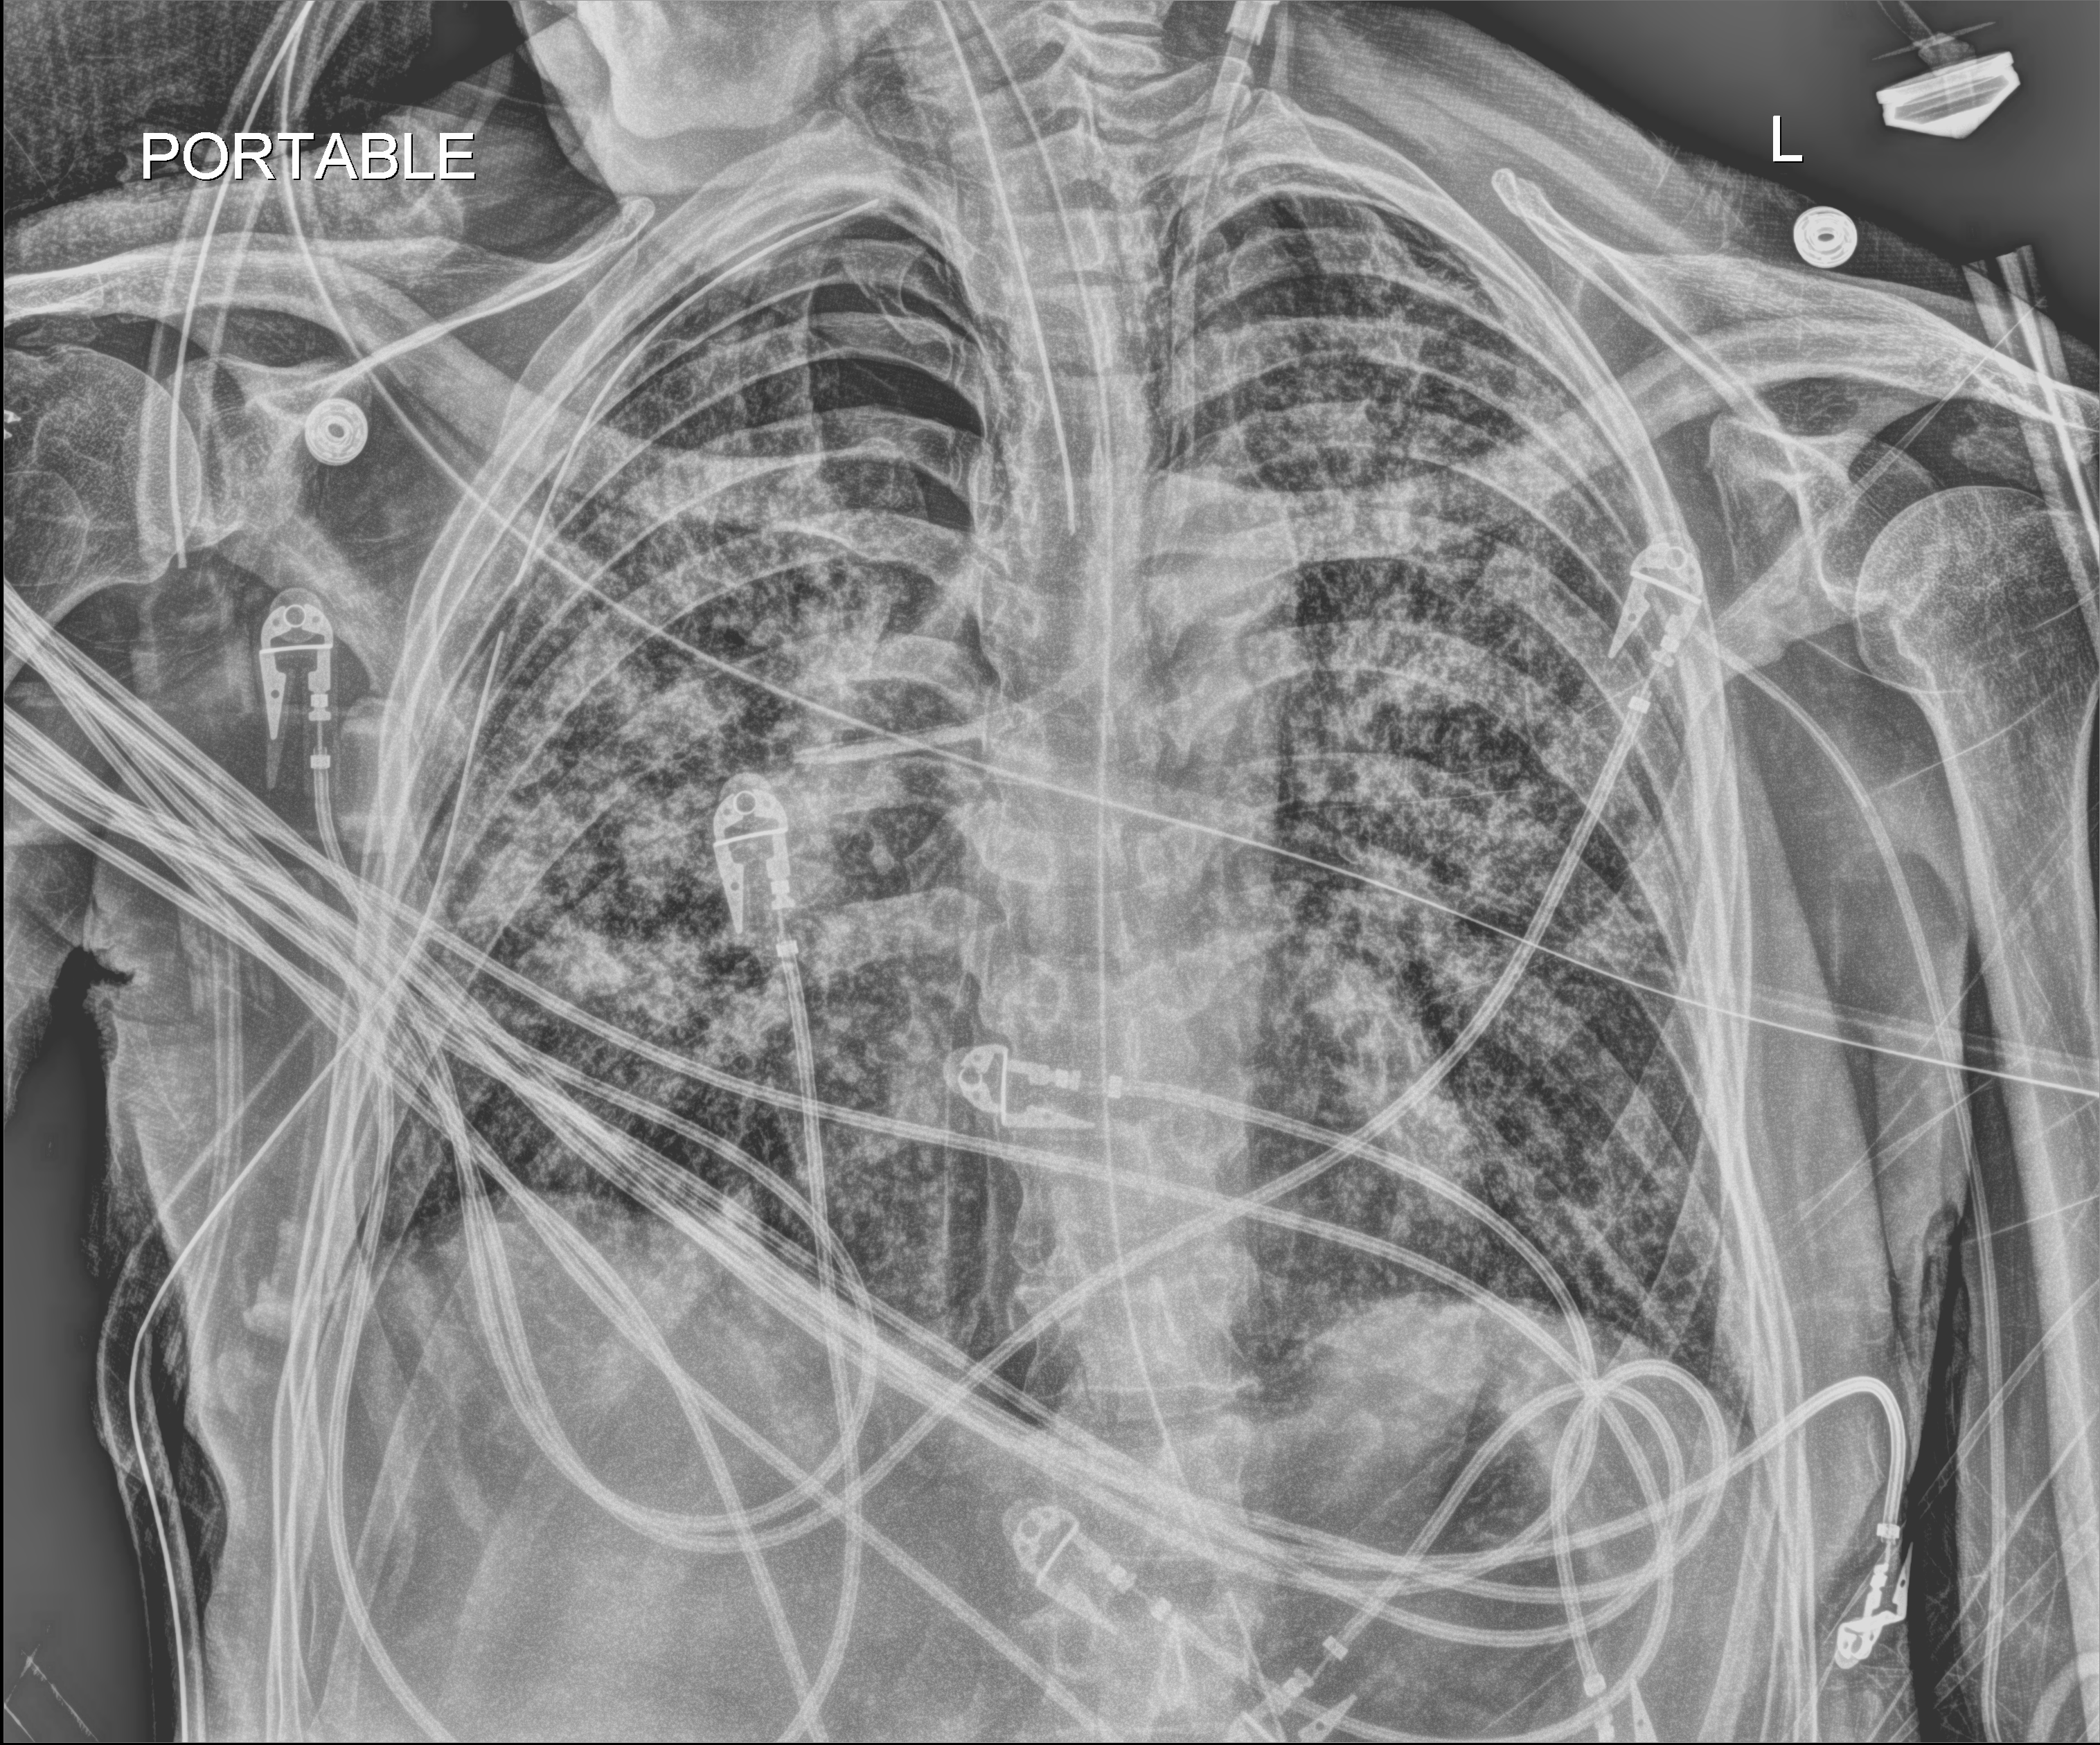
Portable chest radiograph, anteroposterior (AP) projection. Patient hospitalised with COVID-19; male, aged 60–74 years.
From the hospital-stay record, not from the radiograph (when in the stay this image was taken is not recorded): mechanically ventilated during this hospital stay: yes; length of hospital stay: 65 days.